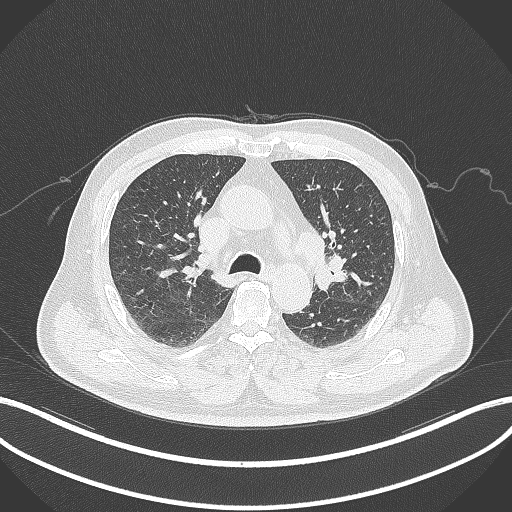
Chest CT, one axial slice; slice 197 of 286 in the series (ordered by position); reconstruction kernel B70f; lung window (W 1500 / L -600 HU); 1 mm slice thickness; 512 × 512 image matrix, field of view 400 × 400 mm. Male patient, age 67 years. Case-level facts recorded for this patient, not image findings: clinical TNM (as recorded): T2a N1 M0.
Annotated regions visible in this slice (rectangle marked by the reading radiologist):
- lung tumour (recorded histology: adenocarcinoma): bounding box (x1, y1, x2, y2) in pixels: (311, 257, 352, 293)